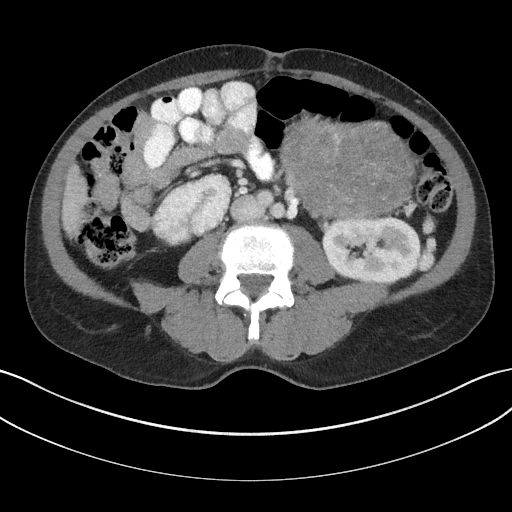
Contrast-enhanced abdominal CT, one axial slice; slice 77 of 147 in the series (ordered by position); reconstruction kernel I31f/3; soft-tissue window (W 400 / L 40 HU); 3 mm slice thickness; 512 × 512 image matrix. Male patient, age 58 years. From the clinical record (not read from this slice): diagnosis: adrenocortical carcinoma; tumour side: left adrenal; tumour size at pathology: 22 cm; Ki-67 index: 26 %; stage (as recorded): 2.
Outlined on this slice (semi-automatic segmentation, software-assisted and operator-edited):
- mass: box from (x=283, y=118) to (x=413, y=218) px